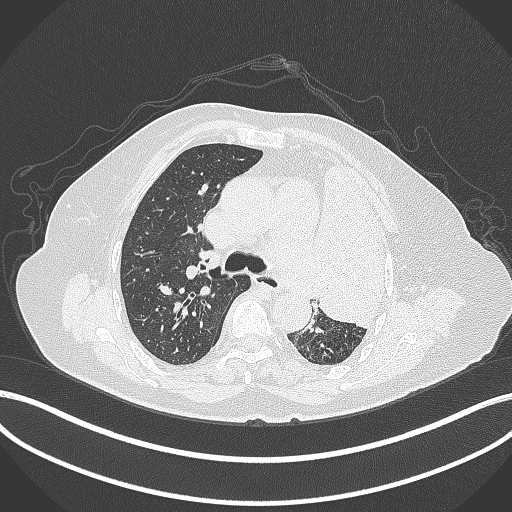
Chest CT, one axial slice; slice 255 of 399 in the series (ordered by position); reconstruction kernel B70f; 120 kVp; lung window (W 1500 / L -600 HU); 512 × 512 image matrix. Patient: female, 75 years. Case-level facts recorded for this patient, not image findings: clinical TNM (as recorded): T3 N3 M1.
Annotated regions visible in this slice (rectangle marked by the reading radiologist):
- lung tumour (recorded histology: adenocarcinoma): bounding box <310,151,395,336> (left, top, right, bottom; pixels)